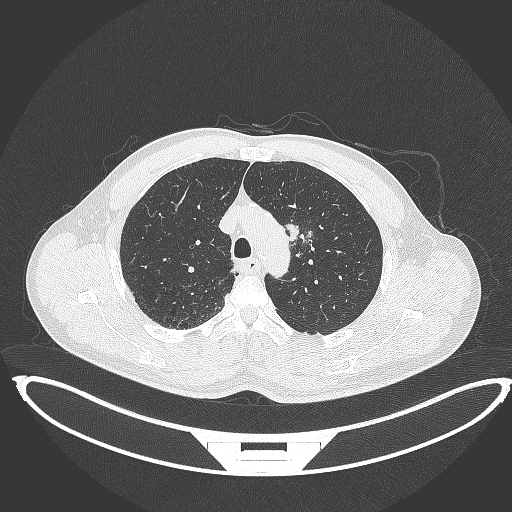
Chest CT, one axial slice; position 330 of 395 along the scan axis; reconstruction kernel B70f; 120 kVp; lung window (W 1500 / L -600 HU); 1 mm slice thickness; 512 × 512 image matrix, field of view 457 × 457 mm. Male patient, age 60 years. From the clinical record (not read from this slice): clinical TNM (as recorded): T2a N0 M0; histopathological grade: G1-G2.
Structures marked on this image (rectangle marked by the reading radiologist):
- lung tumour (recorded histology: squamous cell carcinoma): bounding box (x1, y1, x2, y2) in pixels: (281, 220, 302, 245)